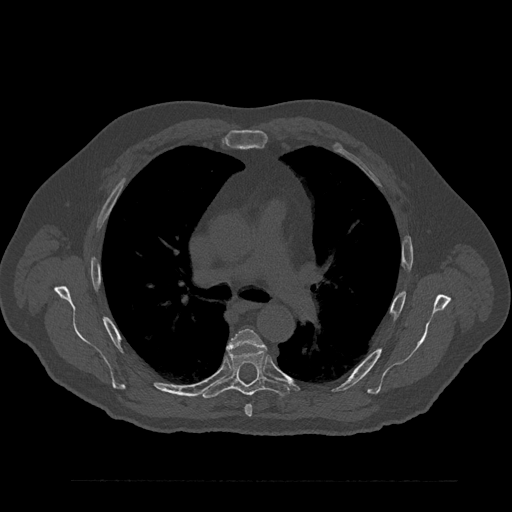
CT including the spine, one axial slice. Slice 570 of 797 in the series (ordered by position). Reconstruction kernel Br40s/3. 120 kVp. Bone window (W 1800 / L 400 HU). 0.5 mm slice thickness. 512 × 512 image matrix, field of view 430 × 430 mm. Patient: male, 61 years. Case-level facts recorded for this patient, not image findings: primary cancer: prostate.
Outlined on this slice (semi-automatically segmented with operator editing):
- T5 vertebra: bounding box (x1, y1, x2, y2) in pixels: (229, 328, 264, 417)
- T6 vertebra: (201, 349, 289, 399)